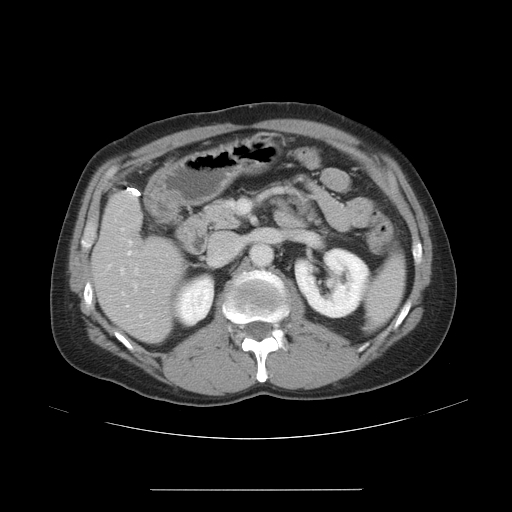
Contrast-enhanced abdominal CT, one axial slice. Slice 23 of 48 in the series (ordered by position). Reconstruction kernel STANDARD. 120 kVp. Intravenous contrast given. Soft-tissue window (W 400 / L 40 HU). 5 mm slice thickness. 512 × 512 image matrix. Male patient, age 56 years. From the clinical record (not read from this slice): diagnosis: colorectal cancer liver metastases, imaged before liver resection; multiple liver metastases: yes; largest metastasis: 1.8 cm; disease in both lobes: yes.
Annotated regions visible in this slice (expert manual segmentation):
- hepatic veins: bounding box (x1, y1, x2, y2) in pixels: (107, 245, 154, 318)
- liver: (92, 195, 183, 343)
- planned liver remnant (the part of the liver to remain after resection): (96, 195, 183, 342)
- portal vein (with intrahepatic branches): (120, 228, 138, 289)